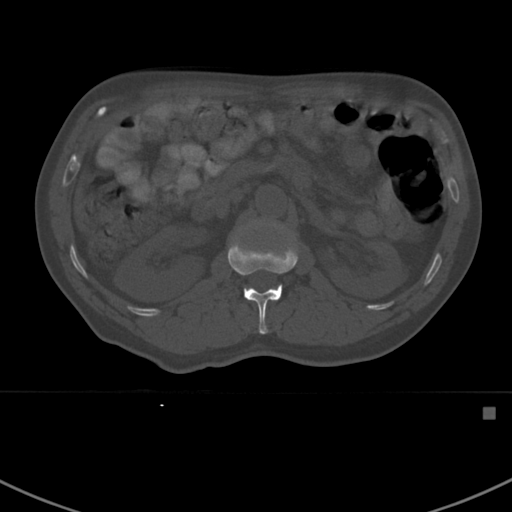
CT including the spine, one axial slice. Position 304 of 412 along the scan axis. Reconstruction kernel Br40s. 120 kVp. Bone window (W 1800 / L 400 HU). 1.5 mm slice thickness. 512 × 512 image matrix, field of view 358 × 358 mm. Male patient, age 59 years. From the clinical record (not read from this slice): primary cancer: prostate.
Annotated regions visible in this slice (semi-automatic segmentation, software-assisted and operator-edited):
- L1 vertebra: bounding box <228,236,298,334> (left, top, right, bottom; pixels)
- L2 vertebra: <246,219,277,228>